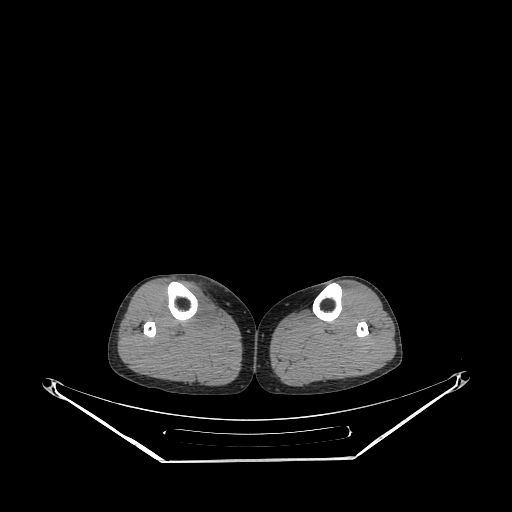
CT of an extremity soft-tissue mass (from a PET/CT study), one axial slice; slice 144 of 267 in the series (ordered by position); 140 kVp; soft-tissue window (W 400 / L 40 HU); 3.75 mm slice thickness; 512 × 512 image matrix, field of view 500 × 500 mm. Female patient. Case-level facts recorded for this patient, not image findings: histological type: undifferentiated – high grade; grade: high; site of the primary tumour: right thigh.
Structures marked on this image (expert contour drawn on MRI and transferred to this co-registered scan by the dataset authors):
- gross tumour volume (mass): bounding box (x1, y1, x2, y2) in pixels: (183, 283, 213, 328)